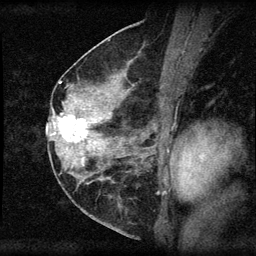
Breast MRI (dynamic contrast-enhanced), one sagittal slice. Position 30 of 60 along the scan axis. Dynamic contrast-enhanced series, image 2 of 3 at this slice position (ordered by acquisition). 1.5 T. TE 4.2 ms, TR 8.2 ms. 2 mm slice thickness. 256 × 256 image matrix, field of view 180 × 180 mm. Patient: female, 45 years.
Outlined on this slice (semi-automatically segmented with operator editing):
- analysis volume of interest (the breast-tissue region the enhancement analysis was run in; not a lesion): bounding box [x1, y1, x2, y2] px = [55, 110, 94, 148]
- tumour enhancement mask (voxels above the 70 % enhancement threshold inside the analysis volume of interest): [58, 115, 87, 143]